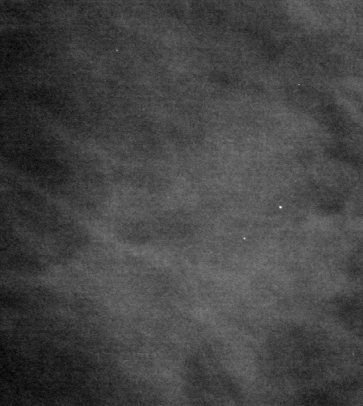
Cropped region of a digitized screen-film mammogram centred on a radiologist-marked abnormality; left breast; MLO view.
Mass, shape irregular, margins spiculated; BI-RADS assessment category 3; benign without callback (not worked up further).